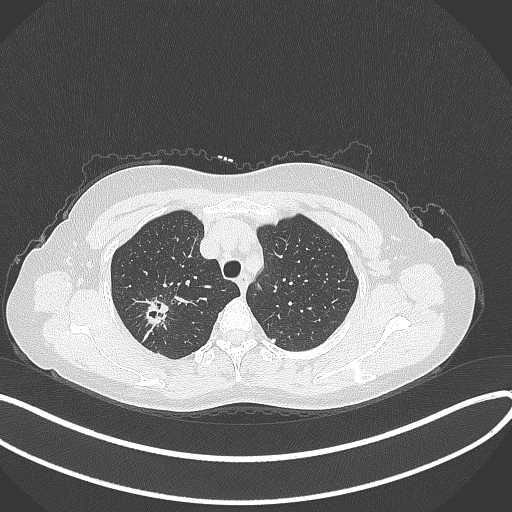
Chest CT, one axial slice; position 292 of 337 along the scan axis; reconstruction kernel B70f; 120 kVp; lung window (W 1500 / L -600 HU); 1 mm slice thickness; 512 × 512 image matrix, field of view 400 × 400 mm. Patient: female, 50 years. From the clinical record (not read from this slice): clinical TNM (as recorded): T1c N0 M0.
Annotated regions visible in this slice (bounding box drawn by a radiologist):
- lung tumour (recorded histology: adenocarcinoma): bounding box (x1, y1, x2, y2) in pixels: (140, 294, 176, 331)